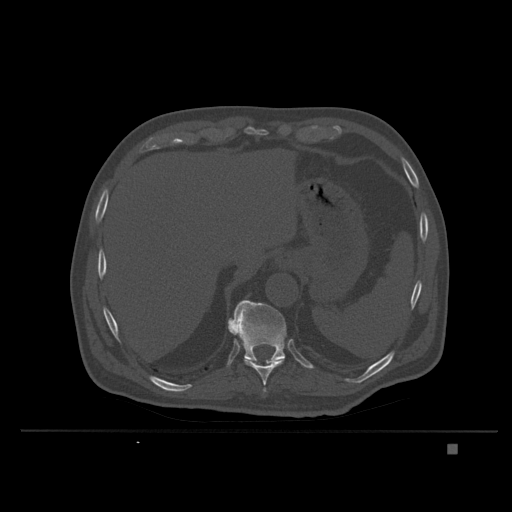
CT including the spine, one axial slice; slice 187 of 435 in the series (ordered by position); bone window (W 1800 / L 400 HU); 512 × 512 image matrix. Male patient, age 73 years. Case-level facts recorded for this patient, not image findings: primary cancer: skin.
Outlined on this slice (semi-automatic segmentation, software-assisted and operator-edited):
- T10 vertebra: box from (x=228, y=324) to (x=285, y=386) px
- T11 vertebra: (x=228, y=300)–(x=286, y=364)
- T9 vertebra: (x=263, y=388)–(x=267, y=394)